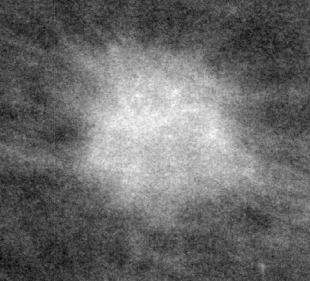
Crop from a digitized film mammogram around one marked abnormality; right breast; CC view.
Mass, shape irregular, margins spiculated; BI-RADS assessment category 4; subtlety rating 5 on a 1 (subtle) to 5 (obvious) scale; pathology result (as recorded, not read from the image): malignant.